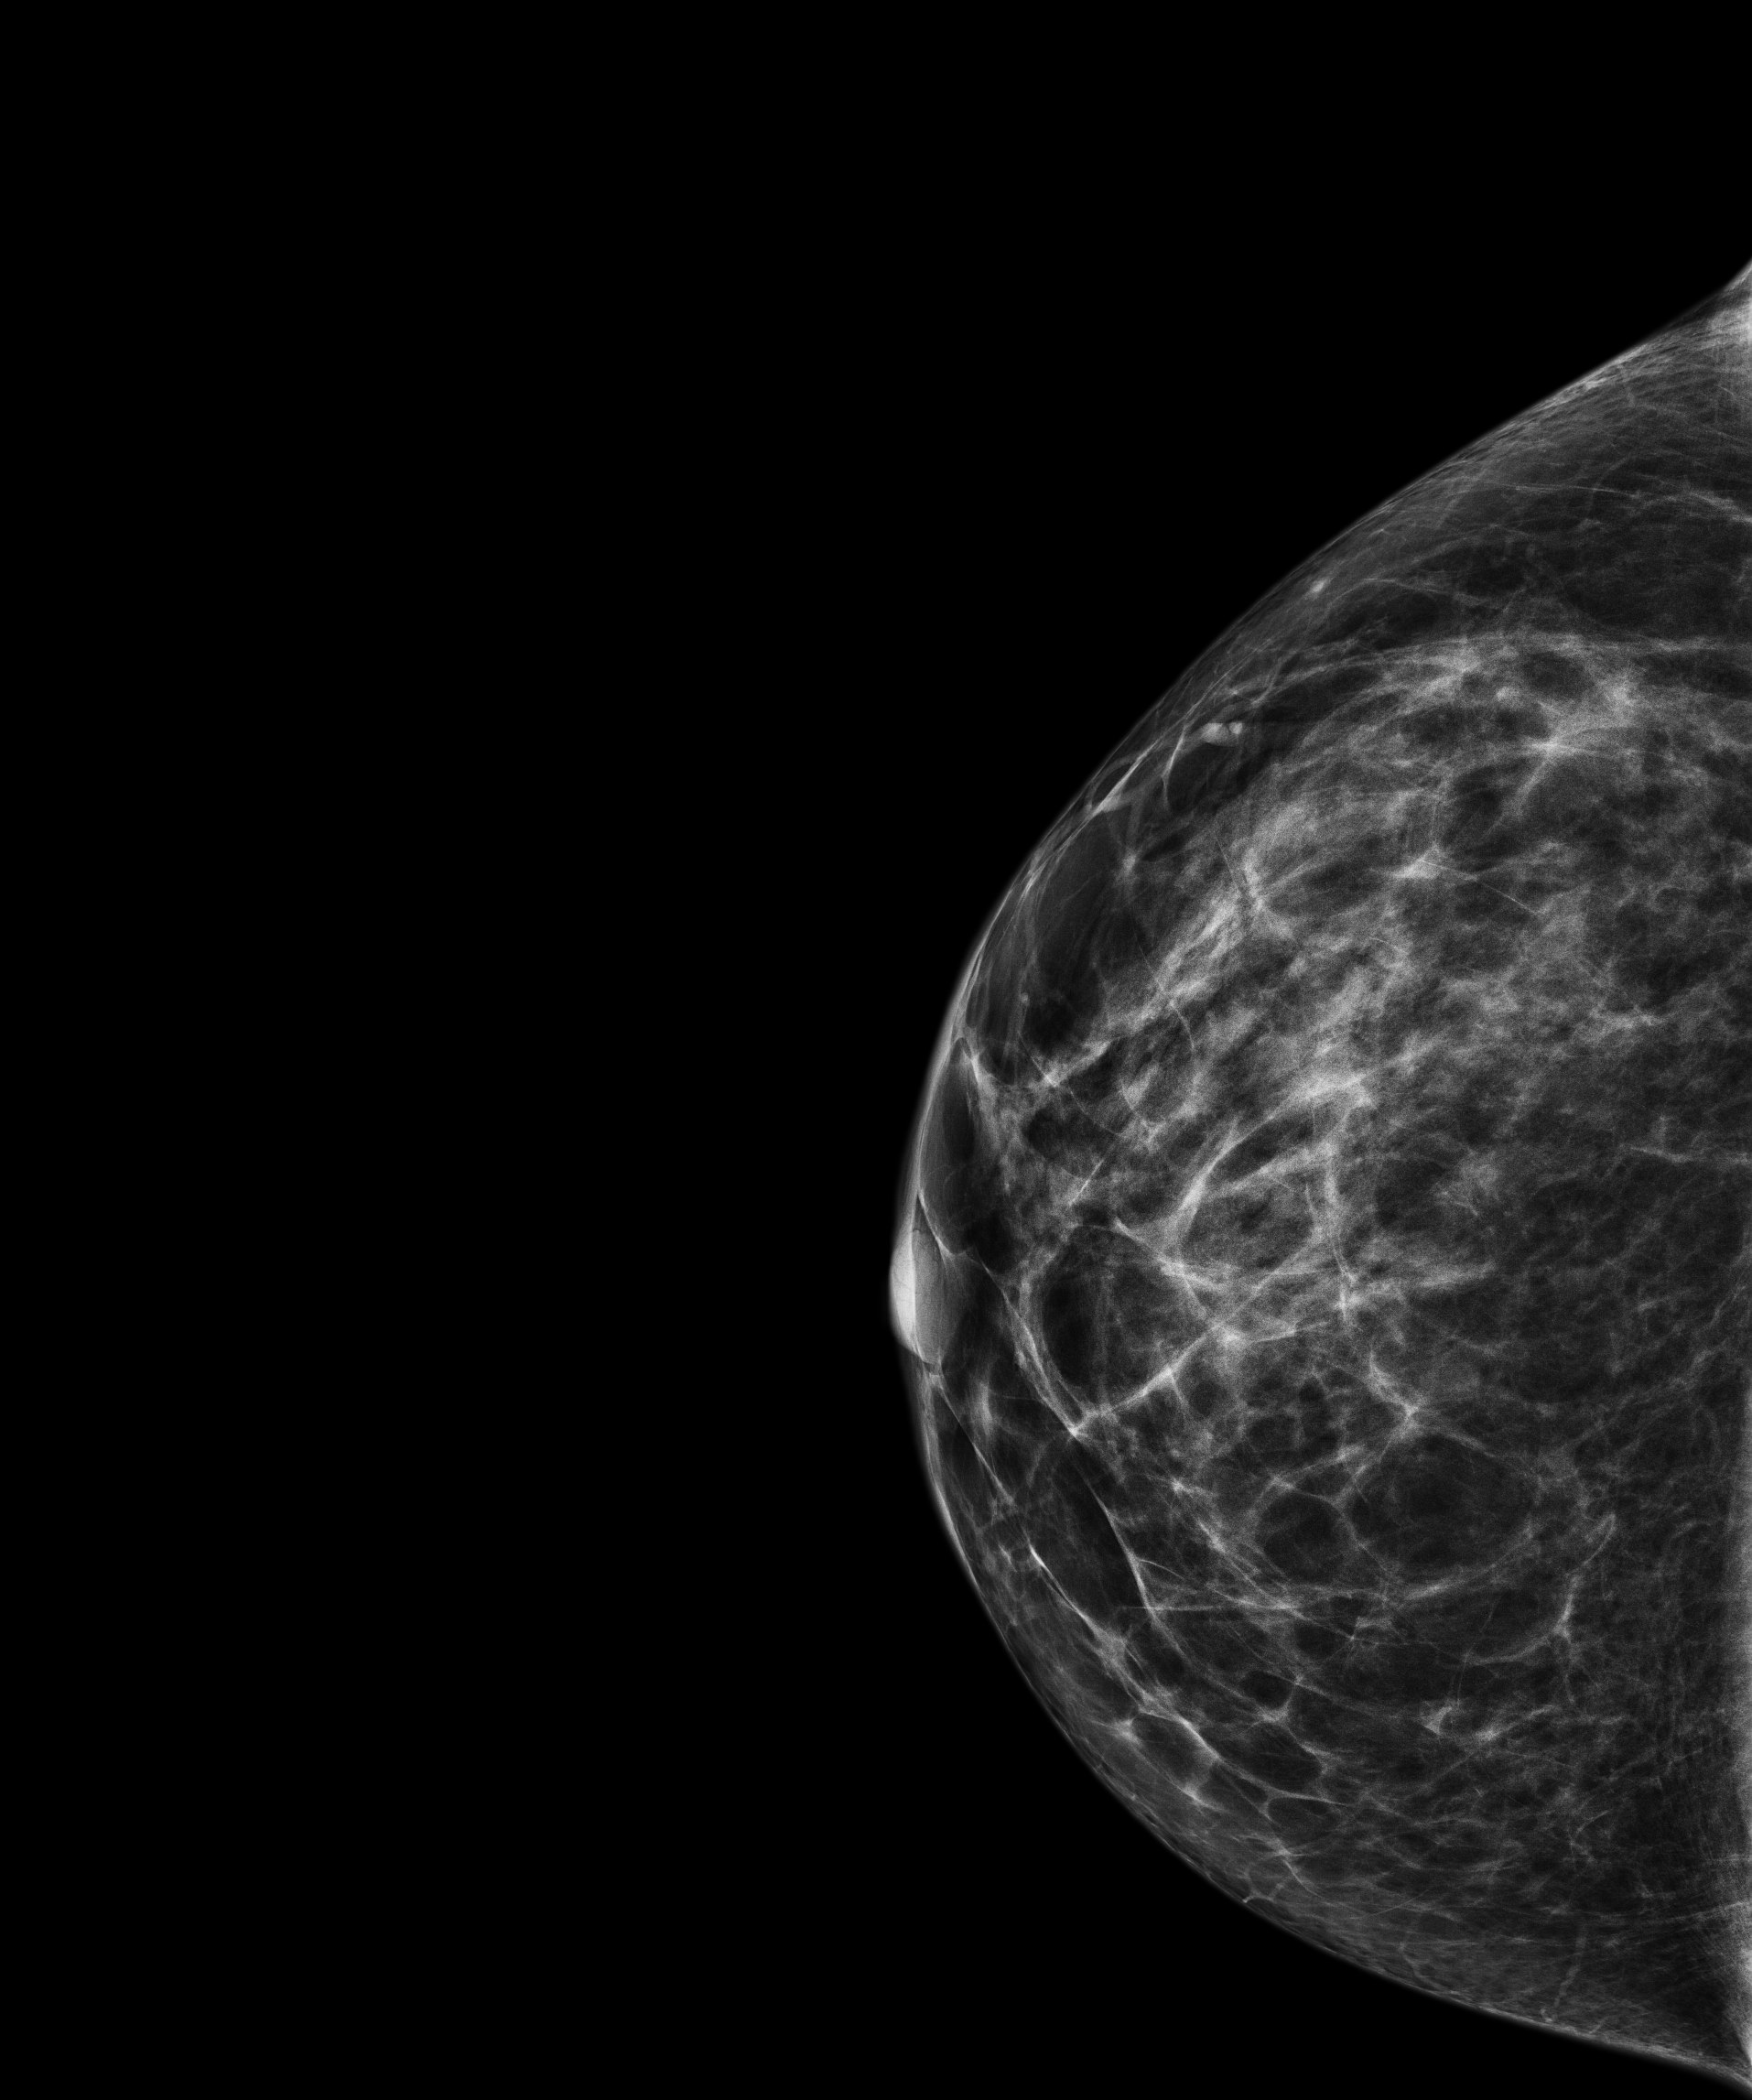
Screening examination; system: Senographe Pristina. Patient aged 46 years (female).
Image type: full-field digital mammogram. Breast: right. Projection: craniocaudal (CC) view.